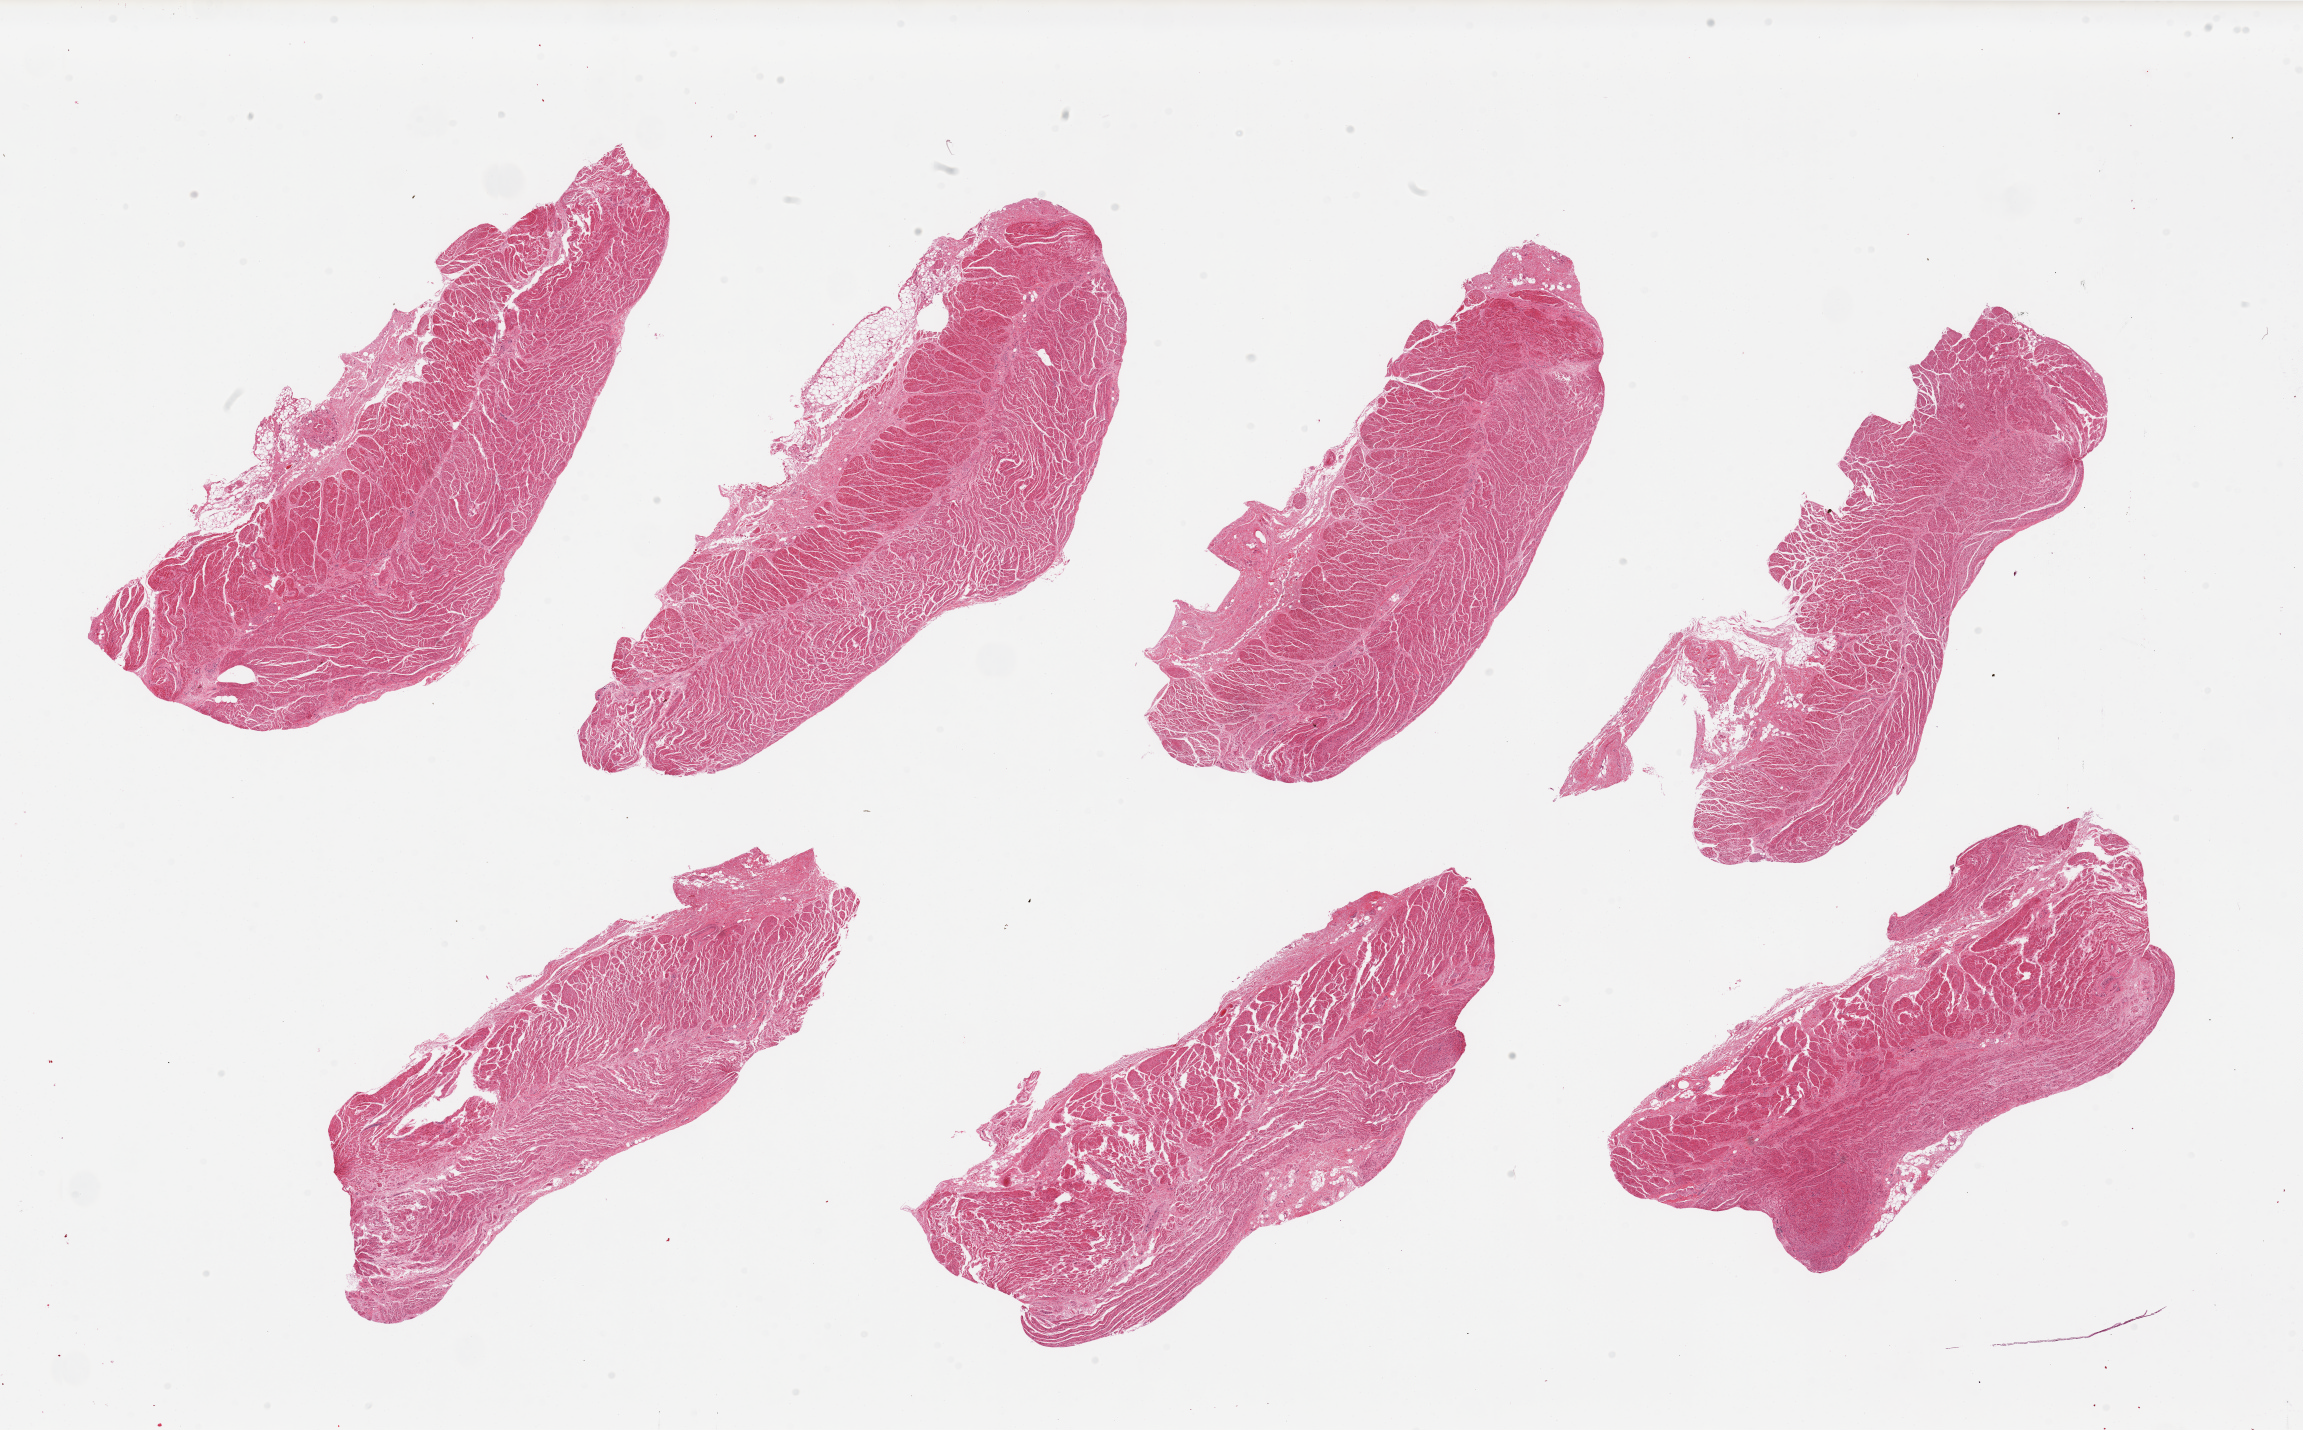
Digitized hematoxylin and eosin (H&E)-stained section, a low-resolution overview of the entire scanned area, about 36.4 x 22.6 mm. PAXgene-fixed paraffin-embedded (PFPE) section. Sampled site (target tissue): gastroesophageal junction. Tissue donor sample.
Pathologist's review note for this sample: 7 pieces, all muscularis, good specimens.